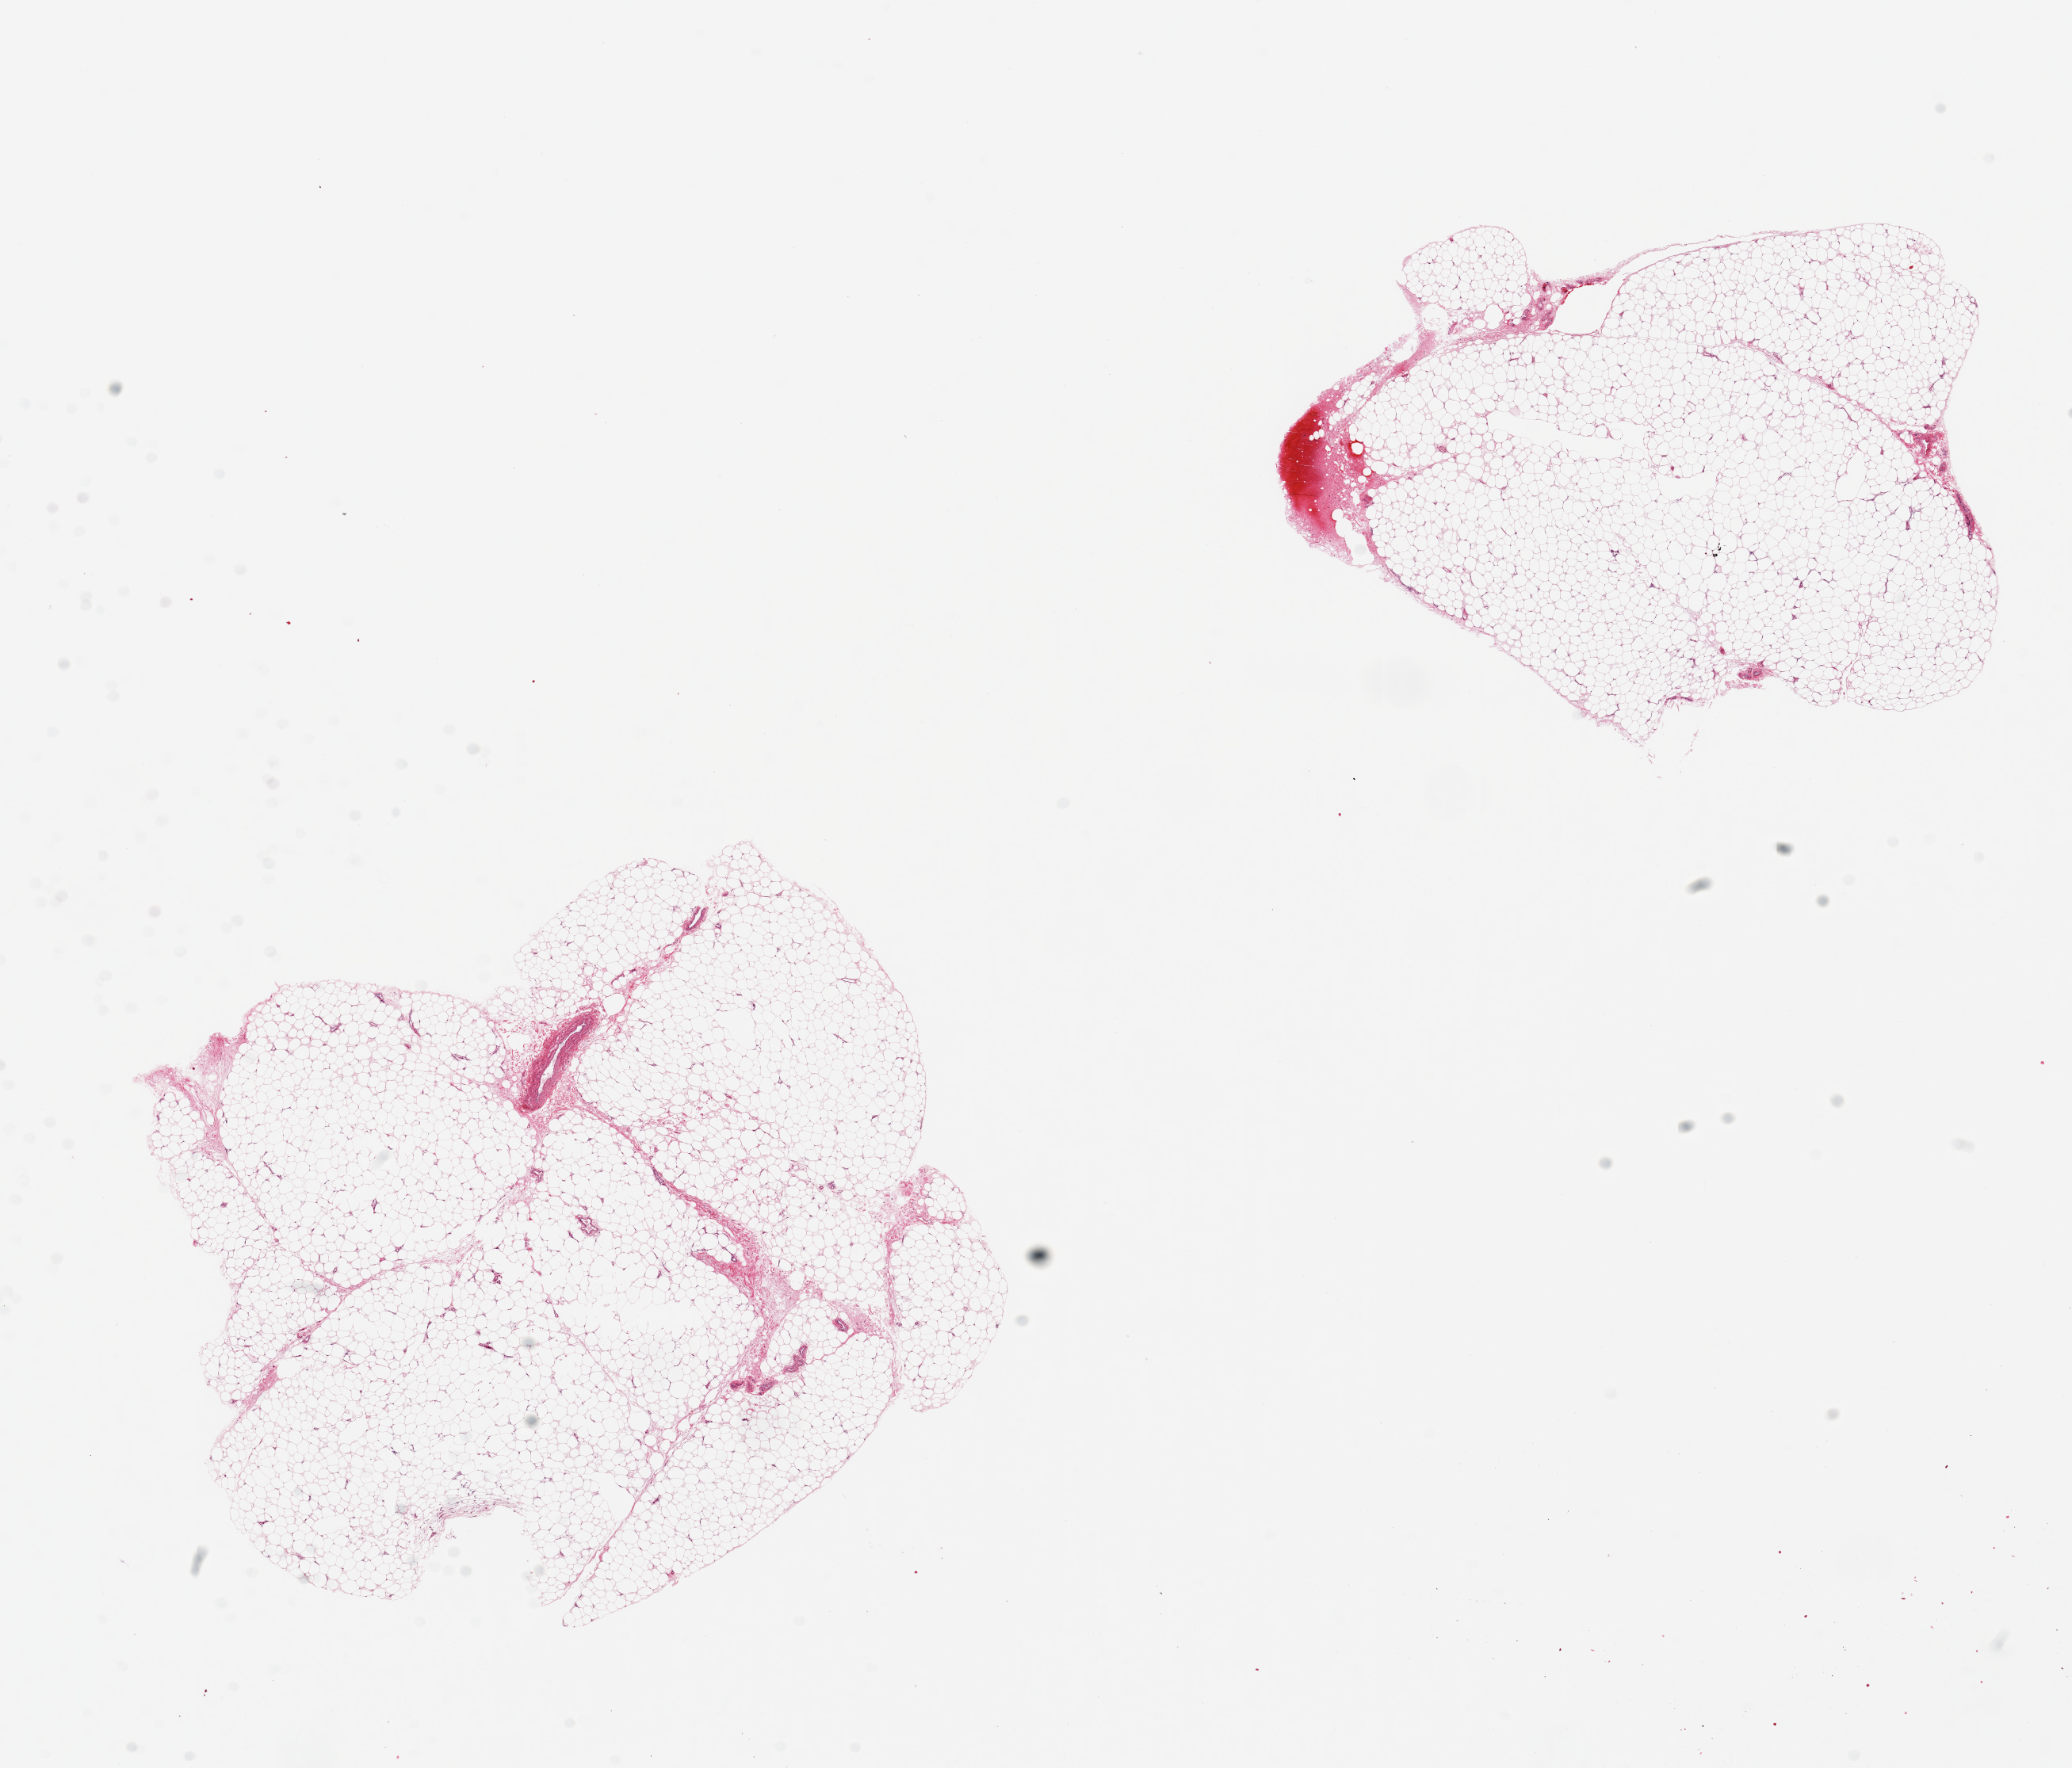
Hematoxylin and eosin (H&E) whole-slide image, a low-resolution overview of the entire scanned area, about 20.7 x 17.6 mm (acquisition: 20x scan). PAXgene-fixed paraffin-embedded (PFPE) section. Sampled site (target tissue): adipose tissue. Donor tissue sample. Male donor.
Reviewer comment on this tissue sample: 2 pieces, 8x7 & 7x7mm; small internal defects.